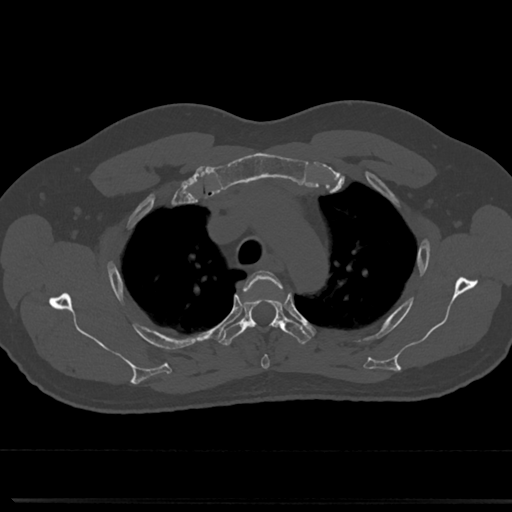
CT including the spine, one axial slice. Position 564 of 817 along the scan axis. Bone window (W 1800 / L 400 HU). 0.5 mm slice thickness. 512 × 512 image matrix, field of view 355 × 355 mm. Male patient, age 61 years. From the clinical record (not read from this slice): primary cancer: prostate.
Annotated regions visible in this slice (semi-automatically segmented with operator editing):
- T3 vertebra: box from (x=245, y=270) to (x=290, y=369) px
- T4 vertebra: (x=219, y=297)–(x=311, y=346)